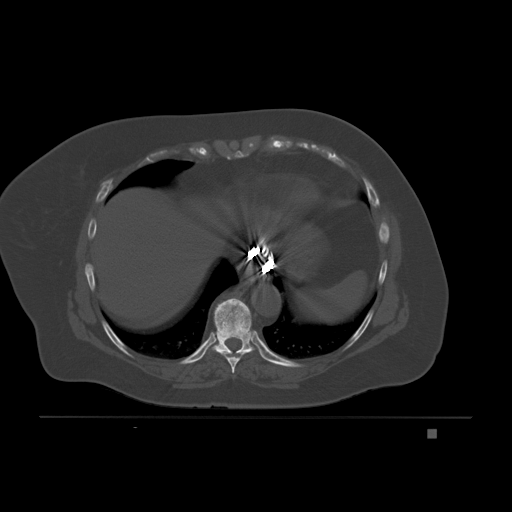
CT including the spine, one axial slice; slice 113 of 221 in the series (ordered by position); bone window (W 1800 / L 400 HU); 3 mm slice thickness; 512 × 512 image matrix, field of view 474 × 474 mm. Female patient, age 63 years. Case-level facts recorded for this patient, not image findings: primary cancer: breast.
Structures marked on this image (semi-automatic segmentation, software-assisted and operator-edited):
- T8 vertebra: box from (x=217, y=350) to (x=252, y=373) px
- T9 vertebra: (x=211, y=298)–(x=264, y=358)